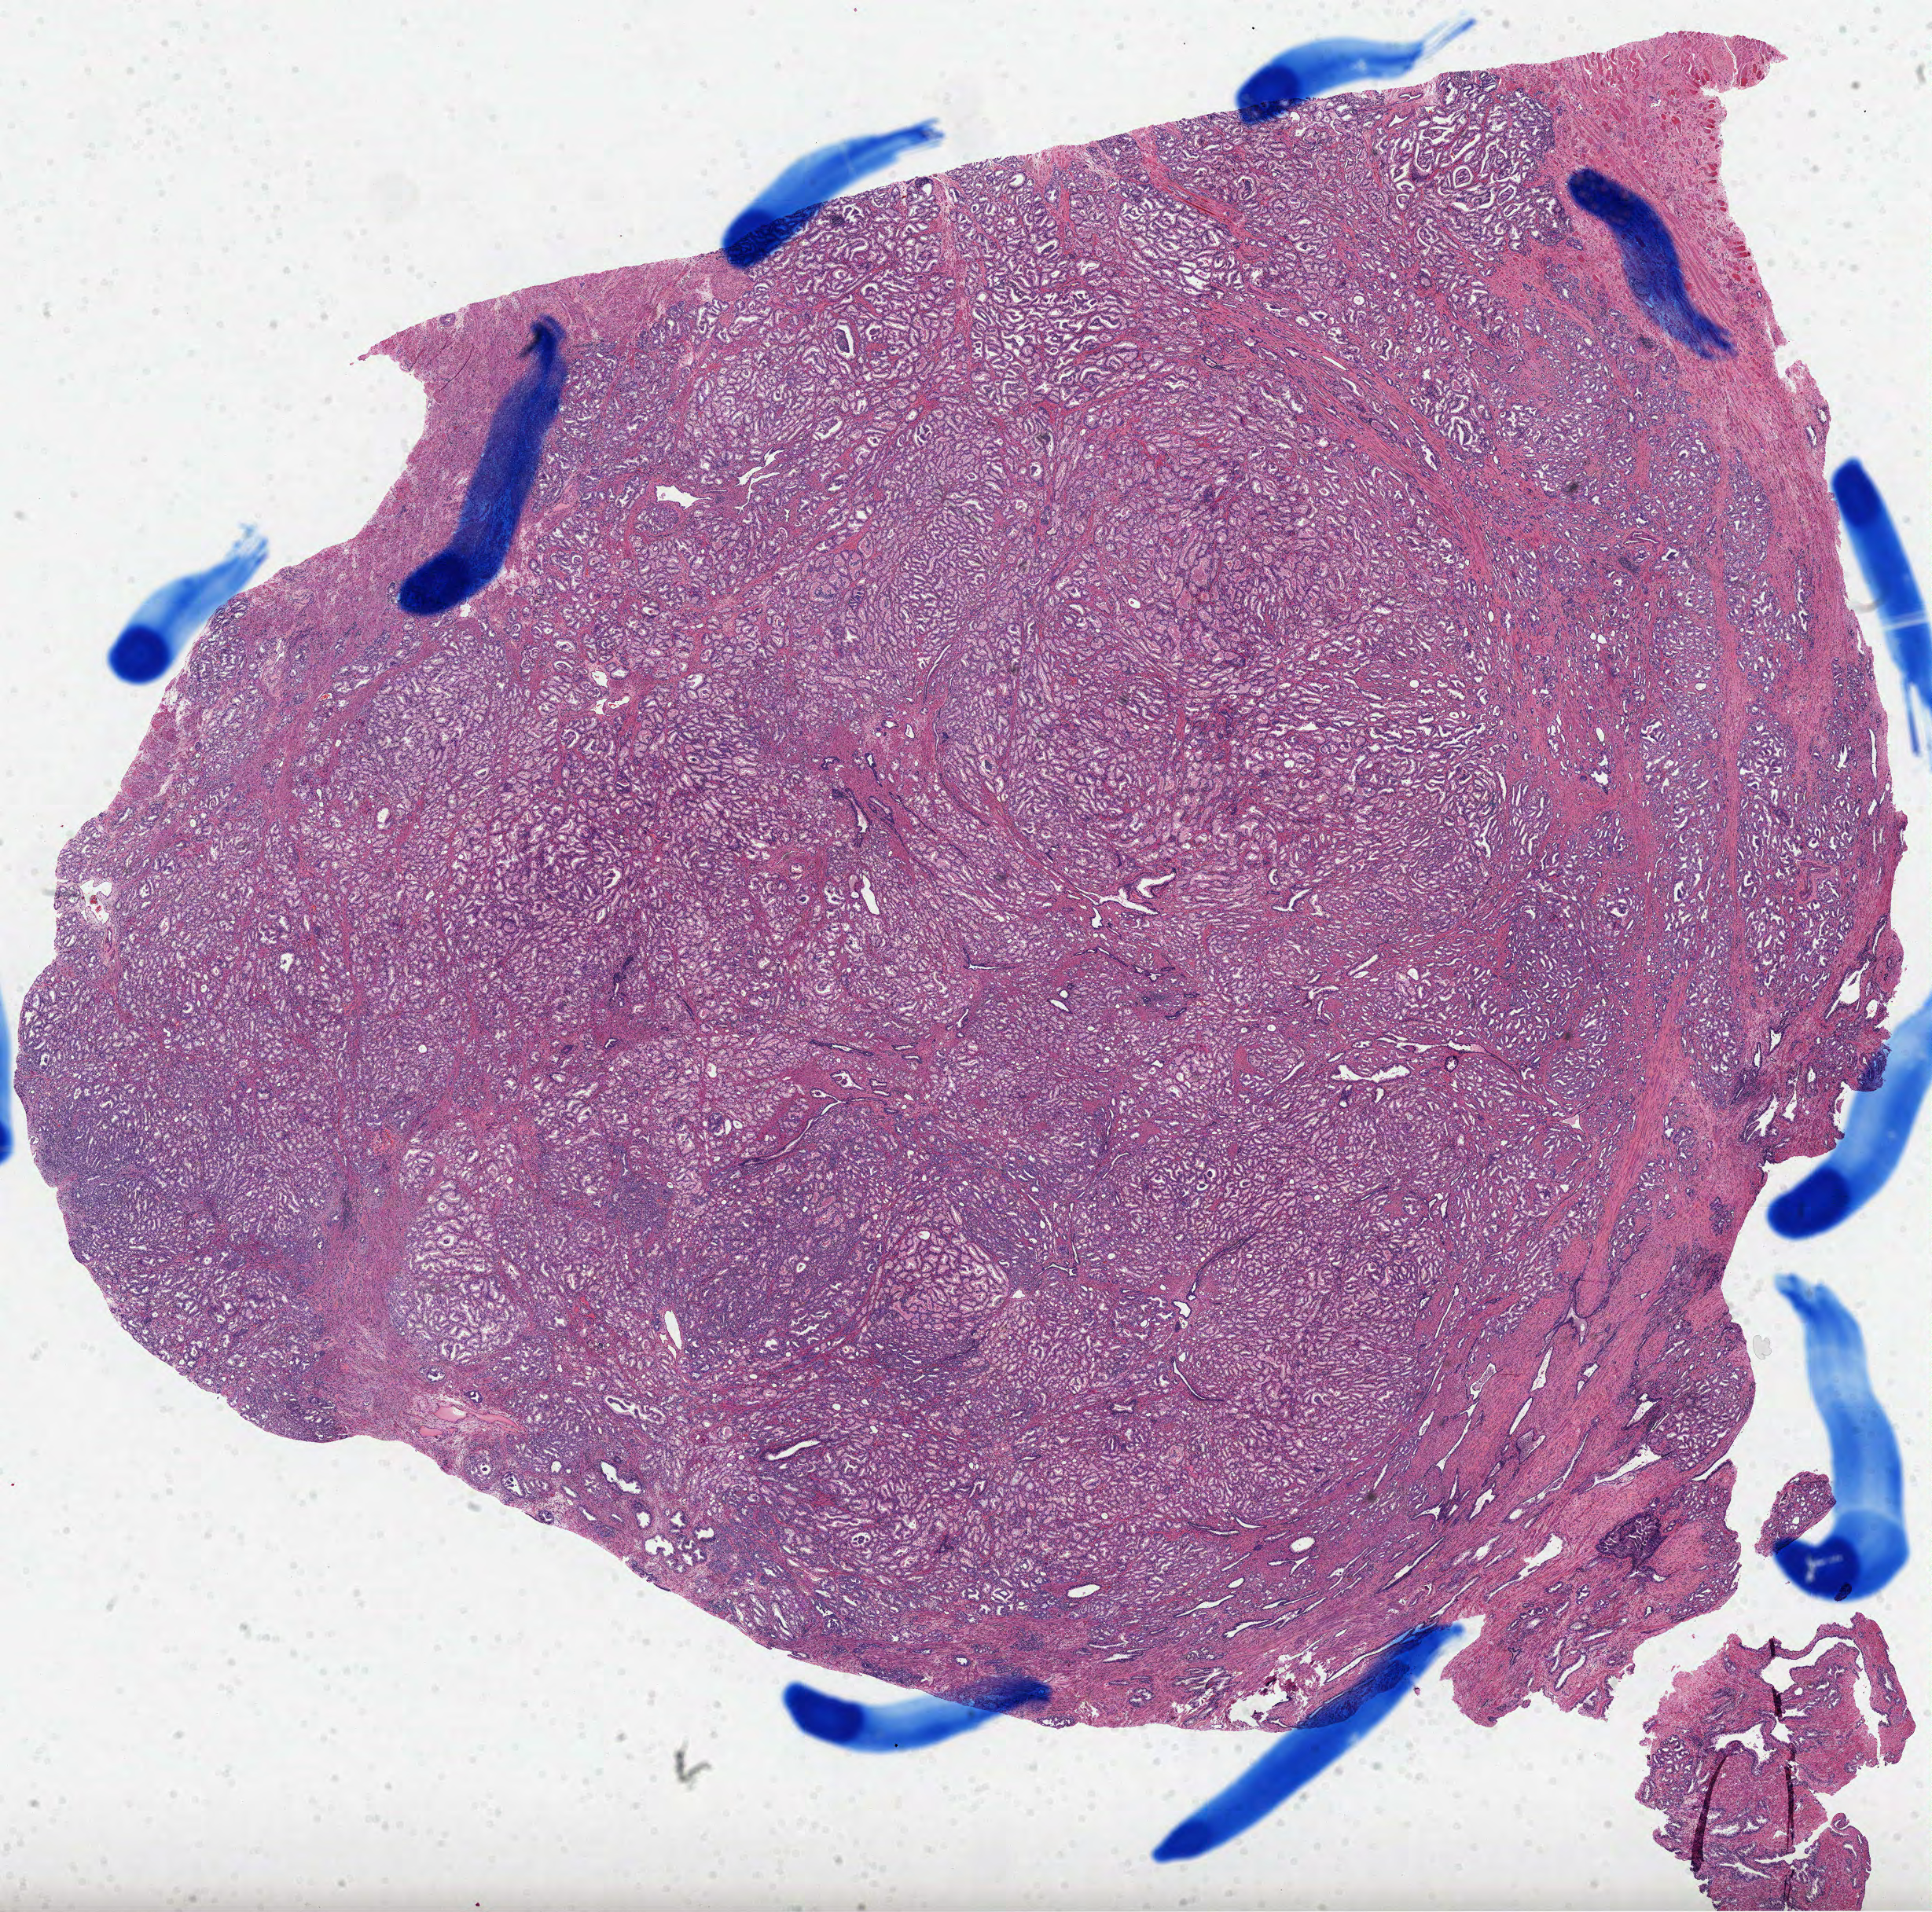
Hematoxylin and eosin (H&E) stained whole-slide image, a low-resolution overview of the entire scanned area, about 19.8 x 19.6 mm (acquisition: 40x scan). Formalin-fixed paraffin-embedded (FFPE) diagnostic section. Sample: primary tumour, prostate. Male, age 57 years at initial diagnosis. Gleason score: 7 (3+4).
Laterality: bilateral. Histologic diagnosis: Acinar cell carcinoma (prostate gland).